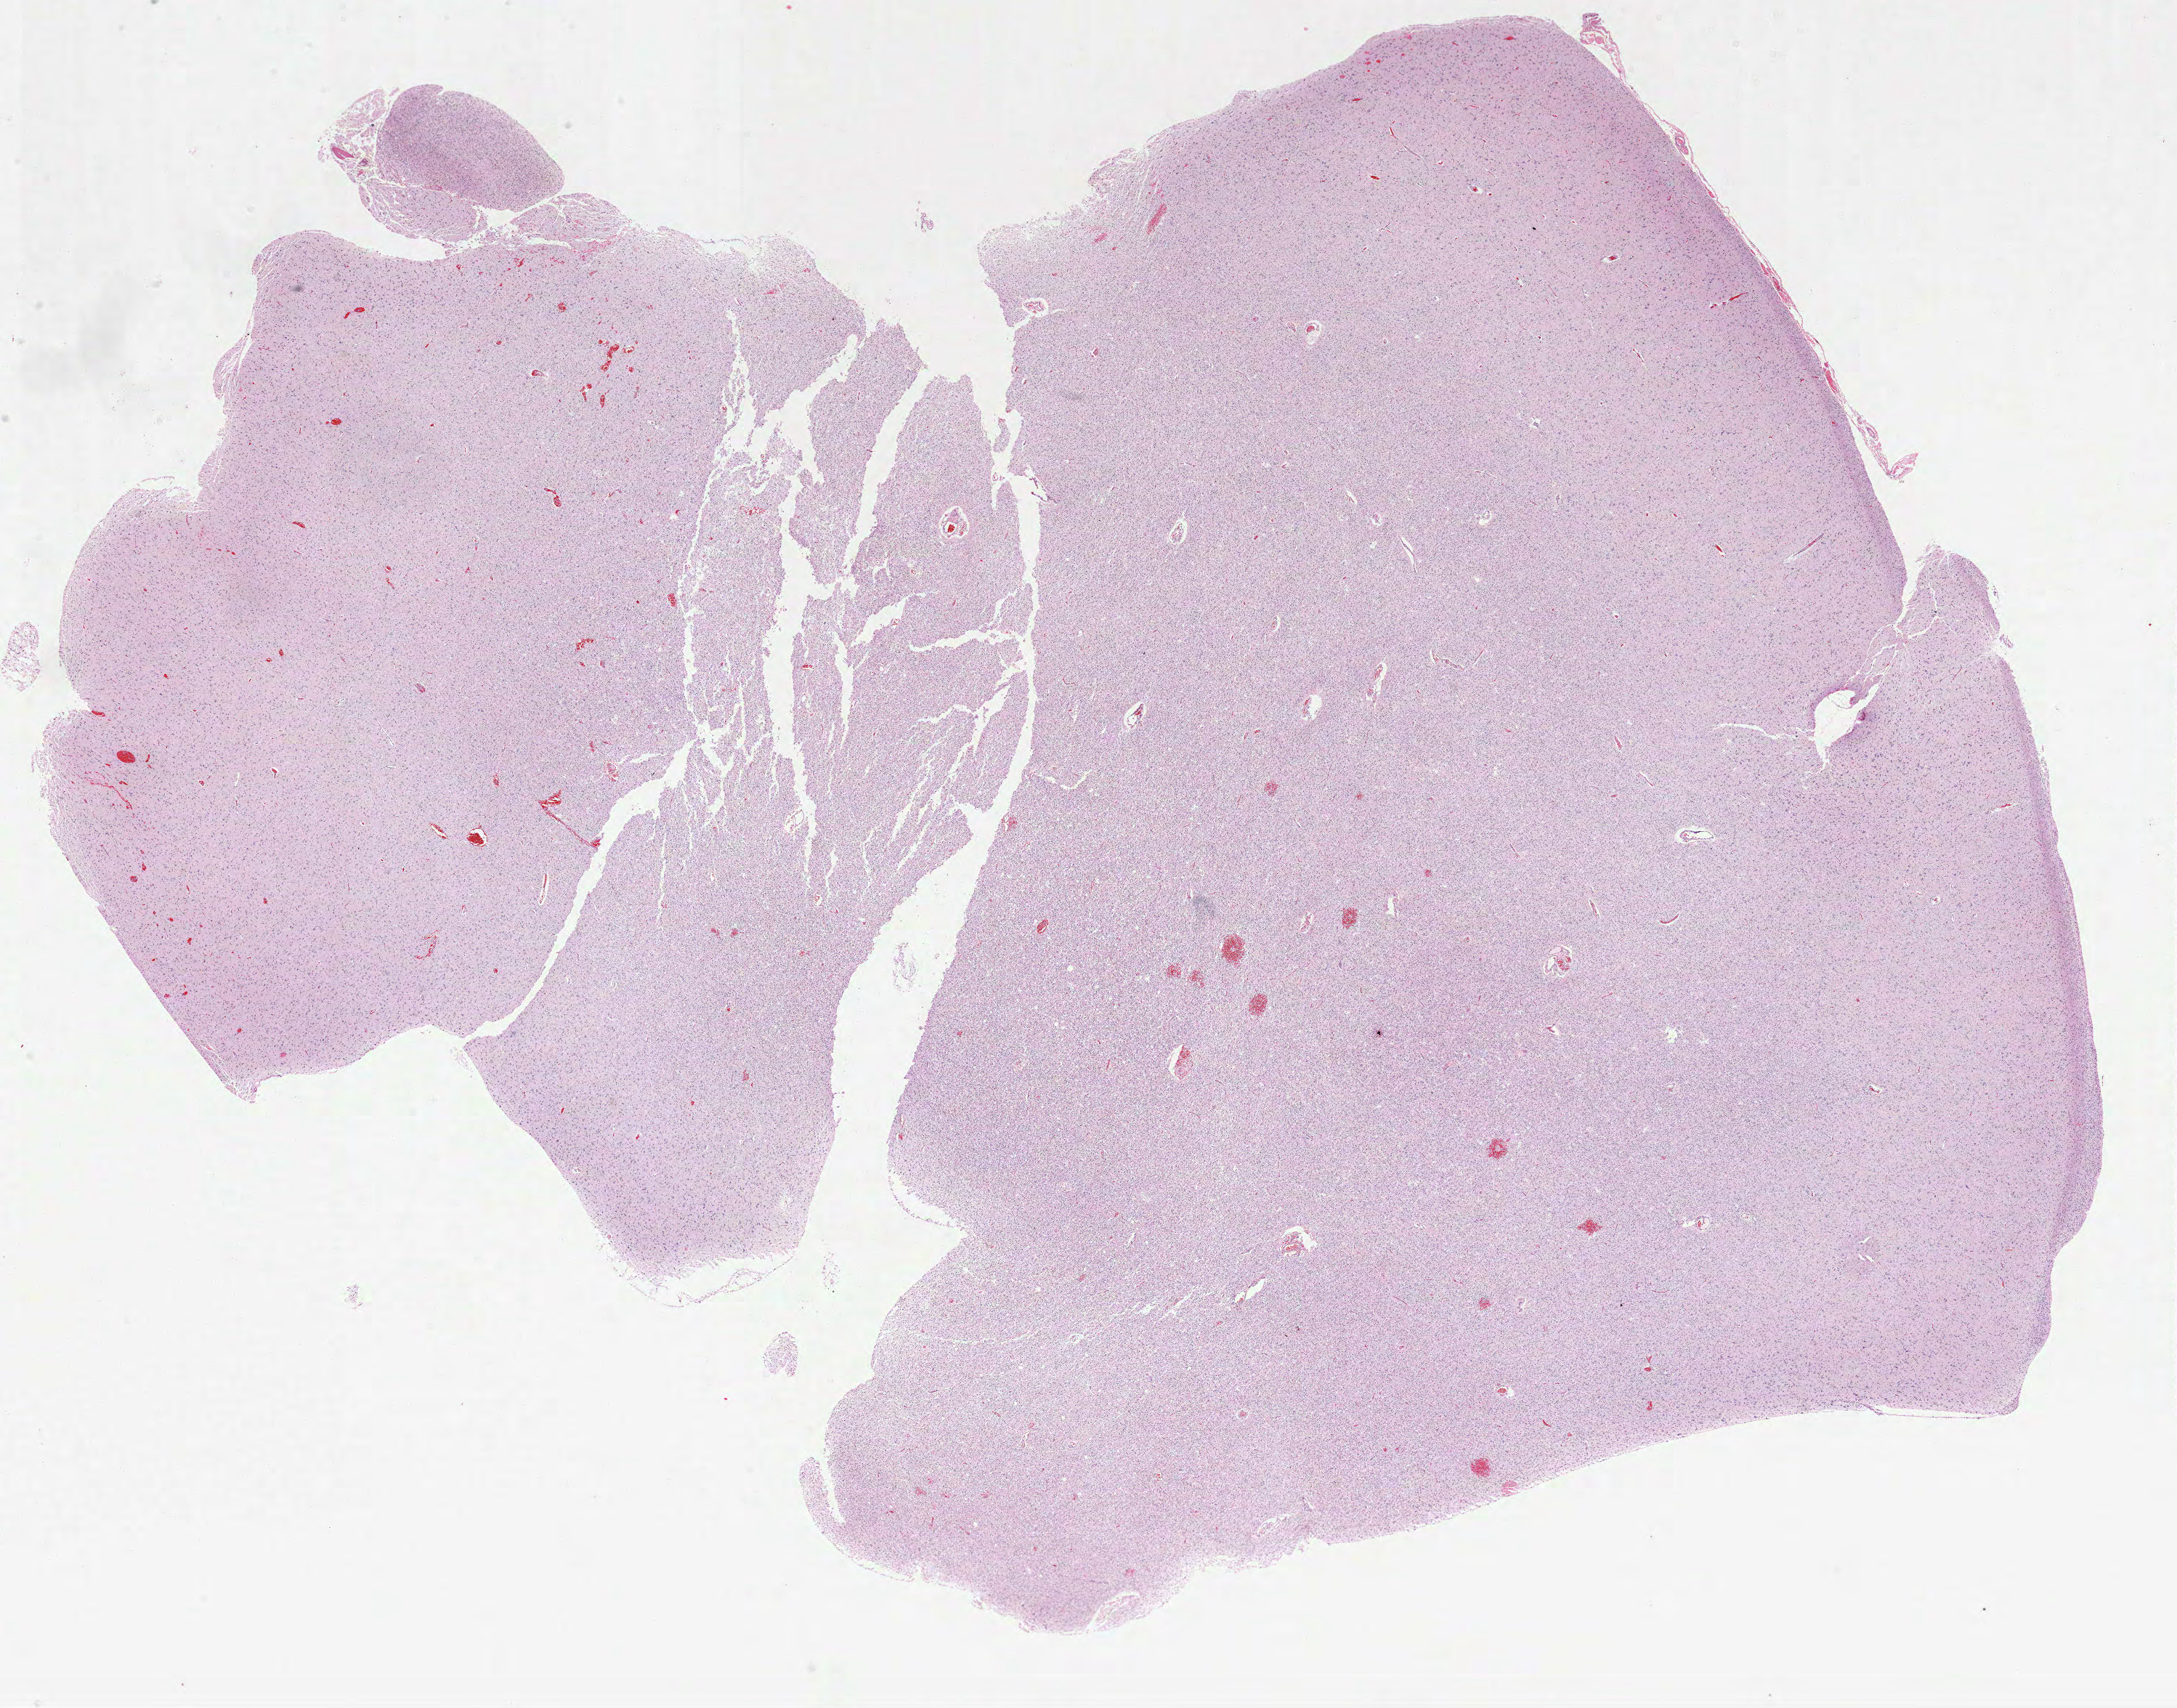
Digitized Hematoxylin and eosin (H&E) stained tissue section (whole slide) — a low-resolution overview of the entire scanned area, about 24.2 x 19.0 mm, formalin-fixed paraffin-embedded (FFPE) diagnostic section, primary tumour sample from the brain. Female, age 45 years at initial diagnosis. Histologic grade: G2 (moderately differentiated).
Histologic diagnosis: Oligodendroglioma, NOS (cerebrum). Laterality: right.